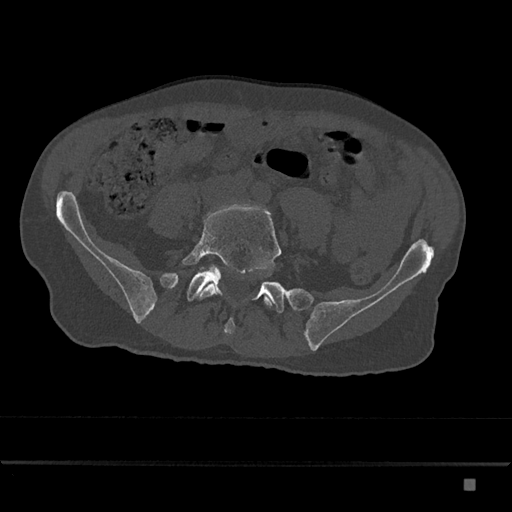
CT including the spine, one axial slice. Position 262 of 797 along the scan axis. Reconstruction kernel Br40s/3. Bone window (W 1800 / L 400 HU). 0.5 mm slice thickness. 512 × 512 image matrix. Patient: male, 72 years. Case-level facts recorded for this patient, not image findings: primary cancer: prostate.
Outlined on this slice (semi-automatic segmentation, software-assisted and operator-edited):
- L5 vertebra: box from (x=182, y=207) to (x=282, y=307) px